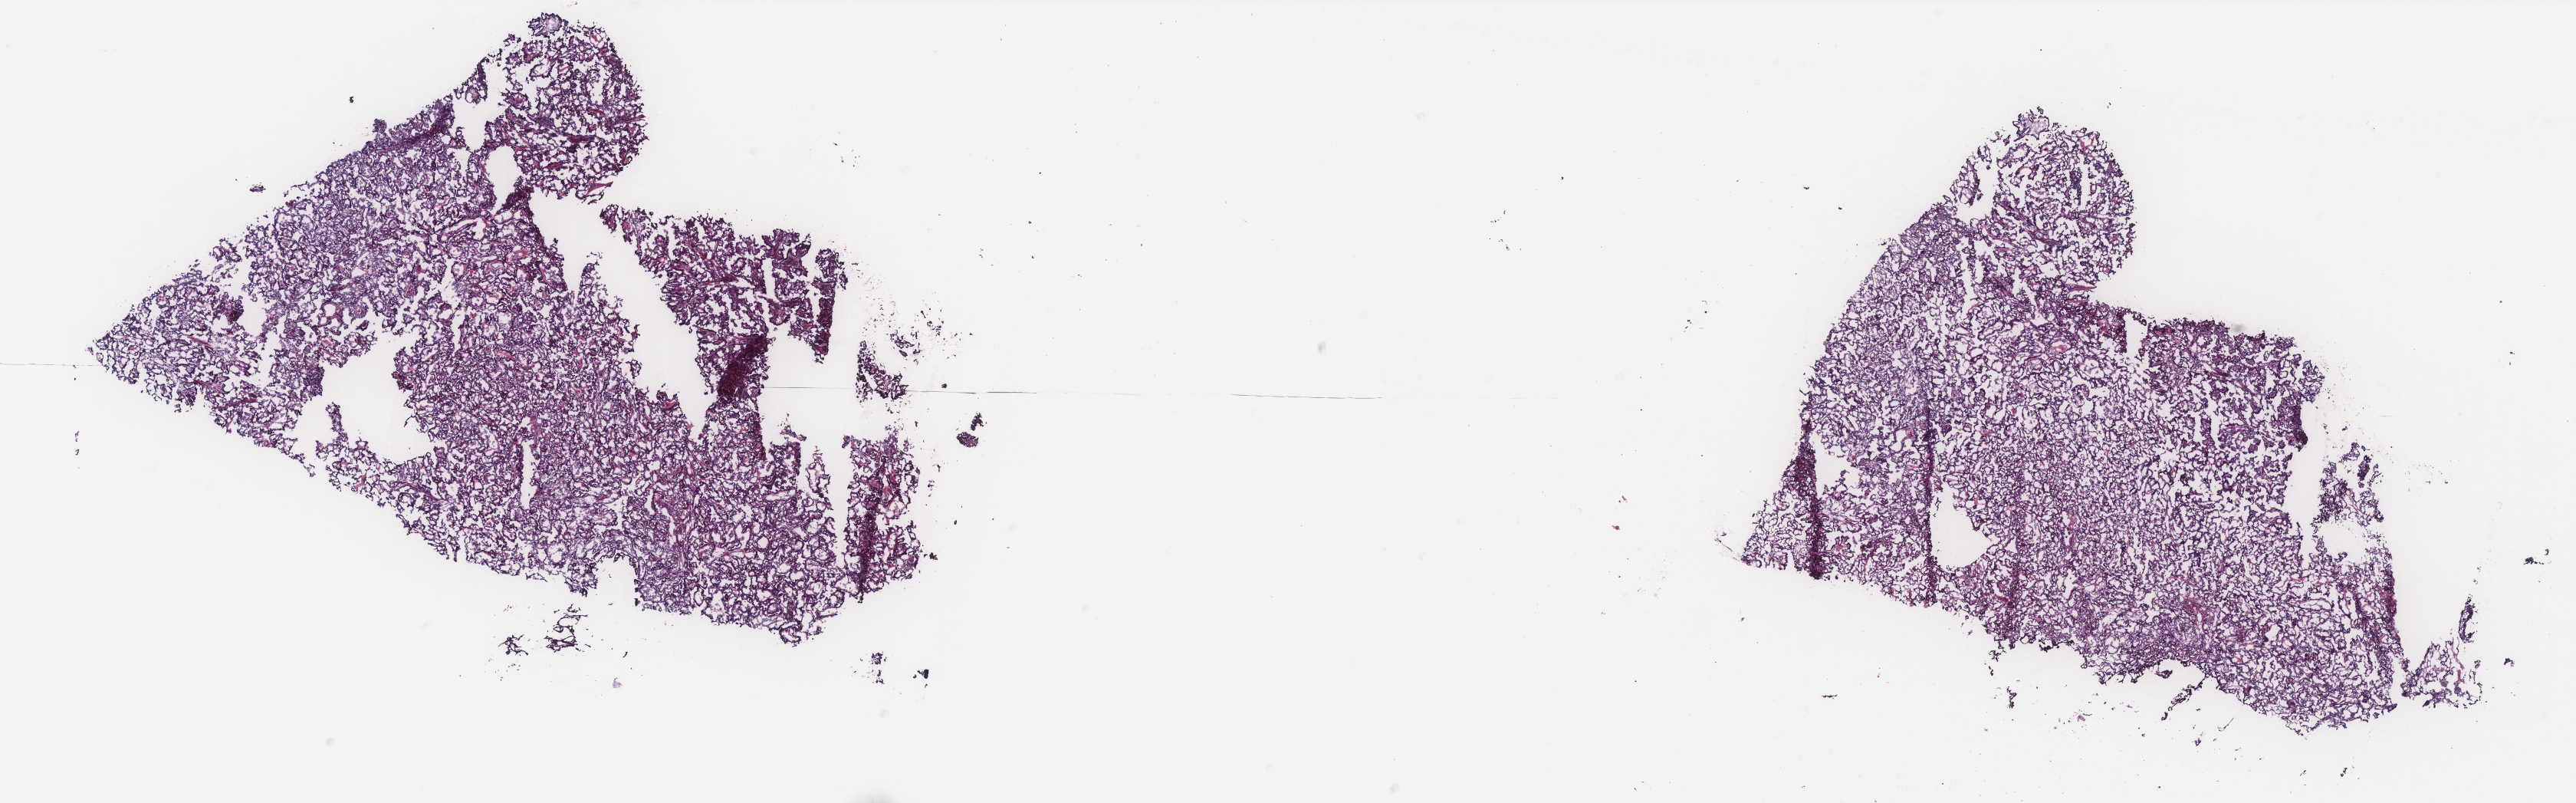
Digitized H&E tissue section (whole slide), a low-resolution overview of the entire scanned area, about 26.9 x 8.4 mm (from a 40x scan); frozen section from the top of the tissue portion; thyroid, primary tumour sample. Female patient; age at initial diagnosis 57 years. Pathologist review of this section (percent, as recorded): tumour cells 80%, tumour nuclei 80%, normal cells 0%, stromal cells 20%, necrosis 0%. Inflammatory infiltration, as recorded: lymphocyte infiltration 2%, monocyte infiltration 1%, neutrophil infiltration 0%.
AJCC pathologic stage: III (7th edition). Lymph nodes positive (case pathology): 0 of 6 examined. Diagnosis: Papillary carcinoma, columnar cell (thyroid gland). Laterality: bilateral.